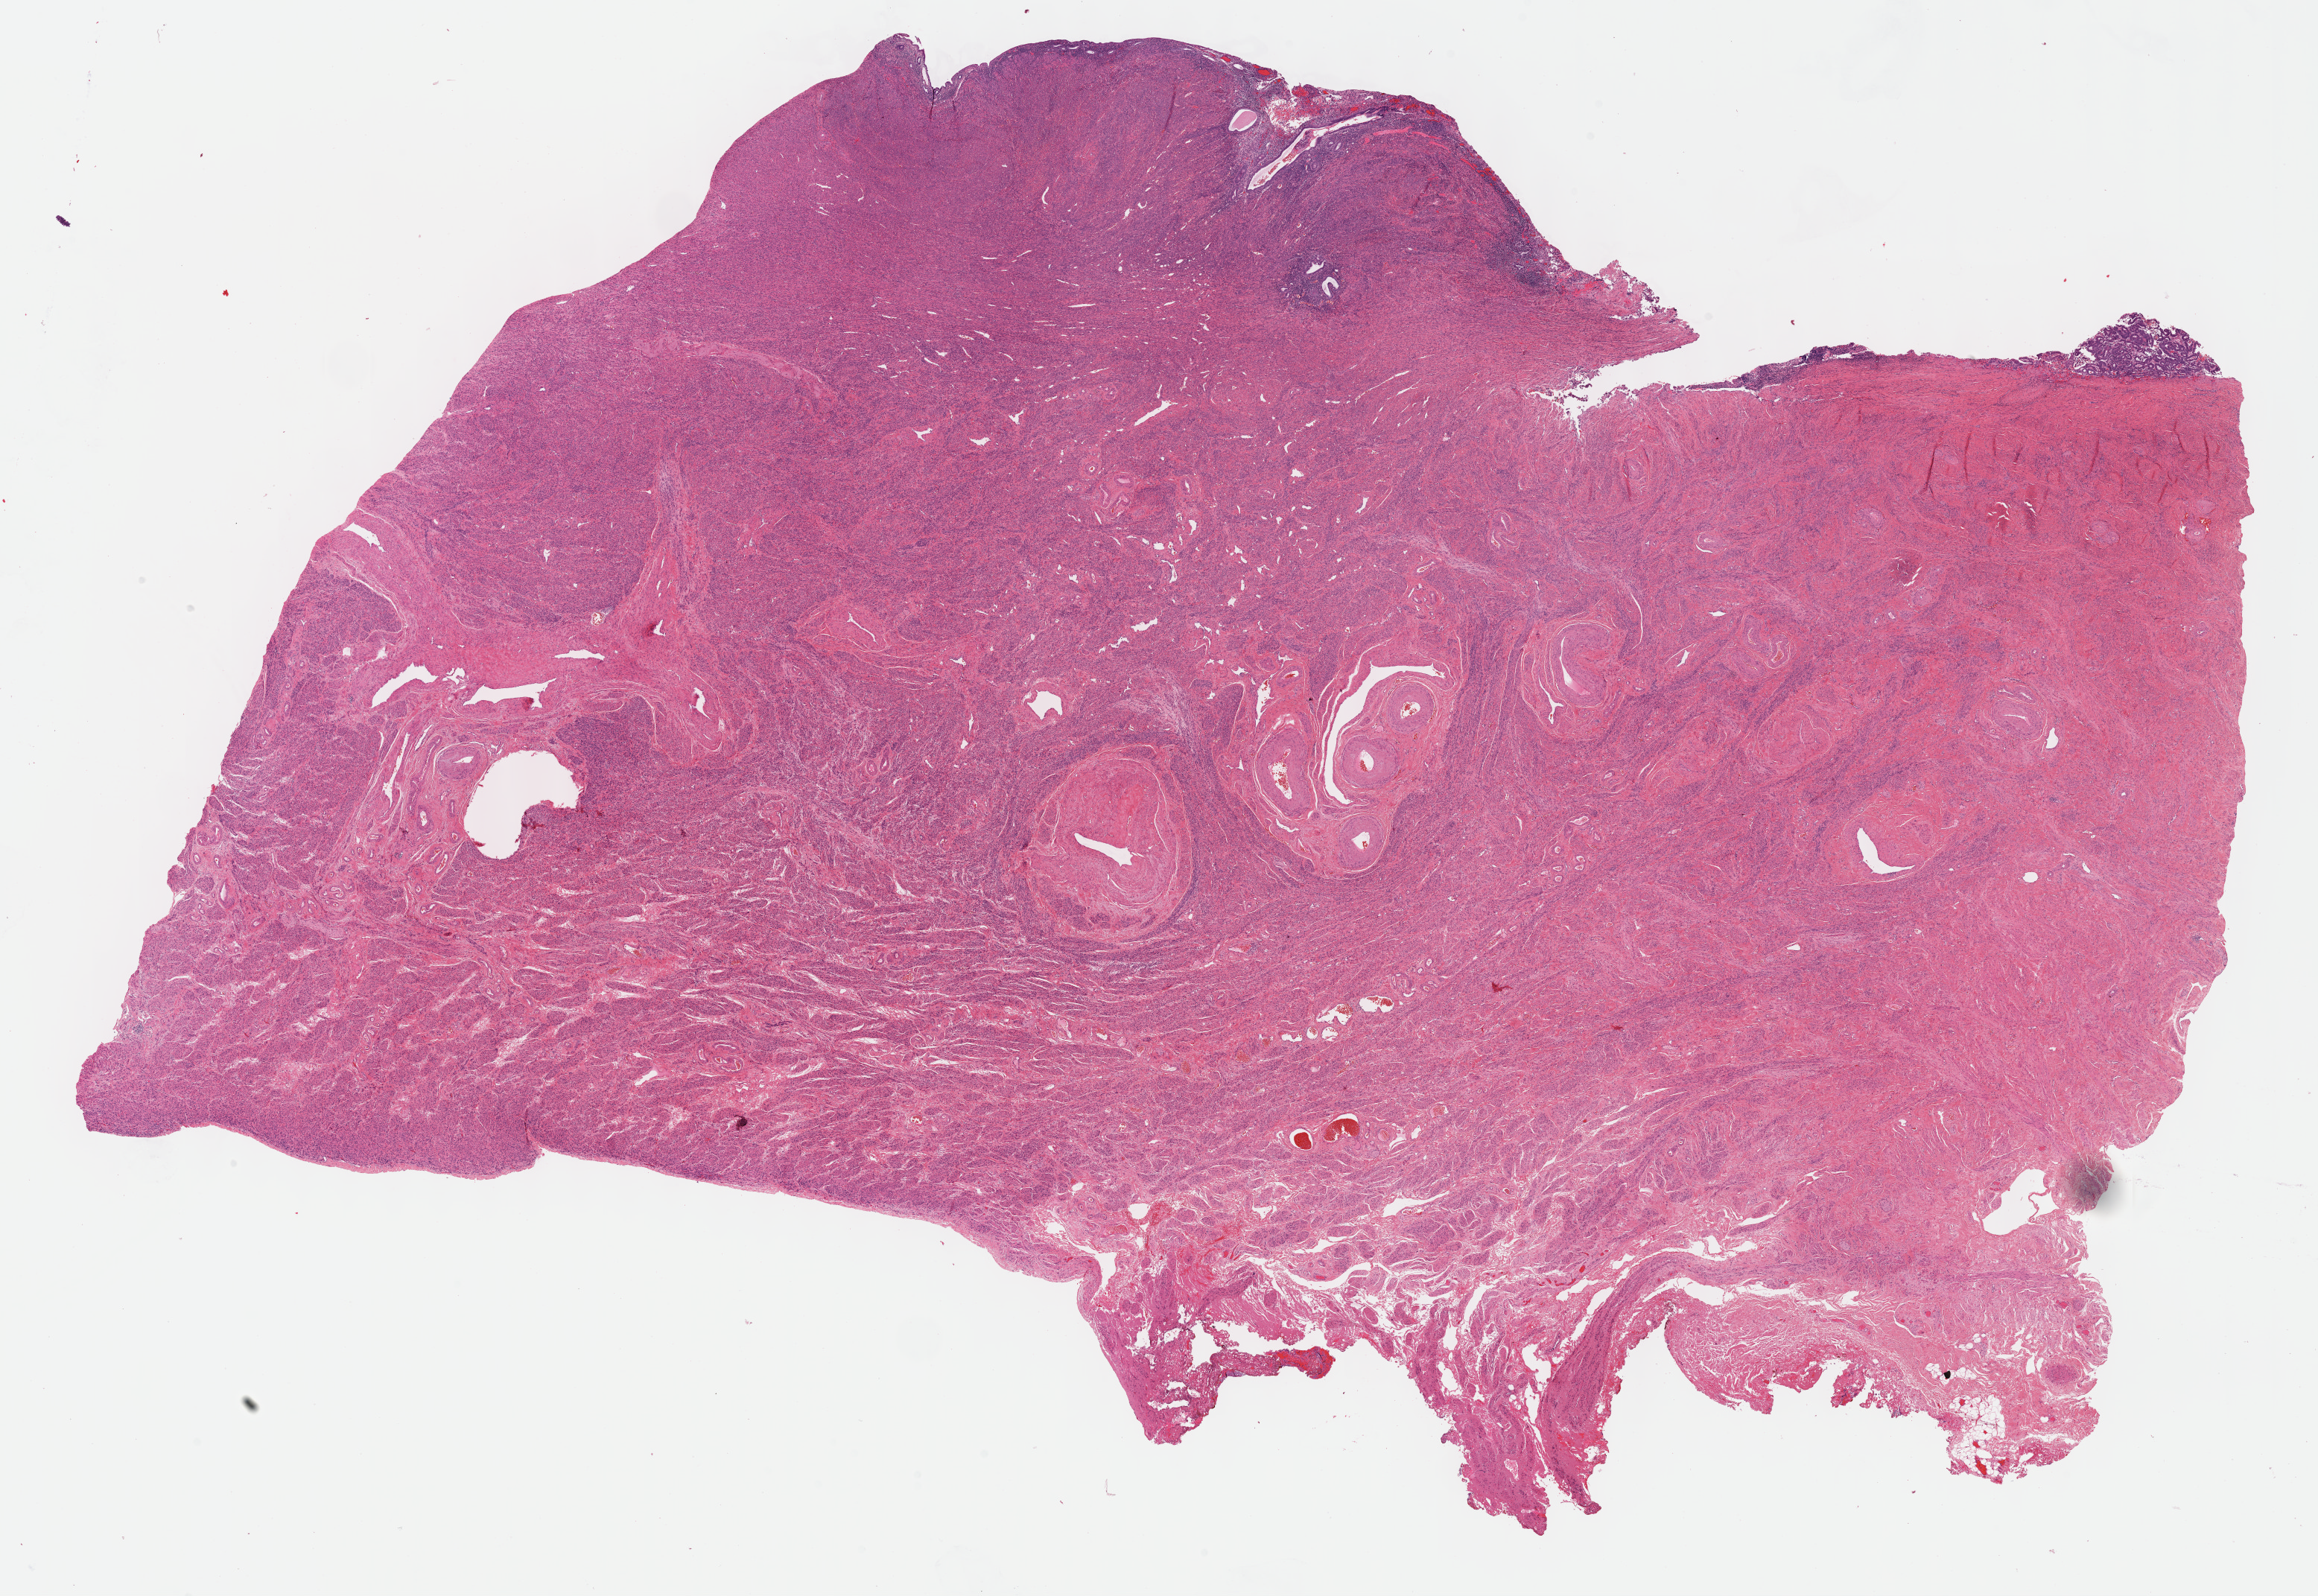
H&E-stained whole-slide image — a low-resolution overview of the entire scanned area, about 25.2 x 17.3 mm (slide scanned at 40x), FFPE section, sample: primary tumour, uterus. Female, age 64 years at initial diagnosis.
Pathologic diagnosis: Endometrioid adenocarcinoma, NOS (endometrium).